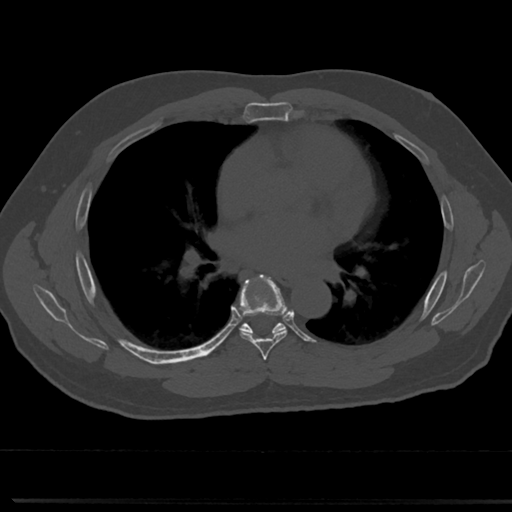
CT including the spine, one axial slice; reconstruction kernel Br40s/3; bone window (W 1800 / L 400 HU); 0.5 mm slice thickness; 512 × 512 image matrix, field of view 355 × 355 mm. Patient: male, 61 years. Case-level facts recorded for this patient, not image findings: primary cancer: prostate.
Outlined on this slice (semi-automatically segmented with operator editing):
- T5 vertebra: box from (x=264, y=369) to (x=273, y=377) px
- T6 vertebra: (x=232, y=277)–(x=308, y=351)
- T7 vertebra: (x=245, y=329)–(x=250, y=332)